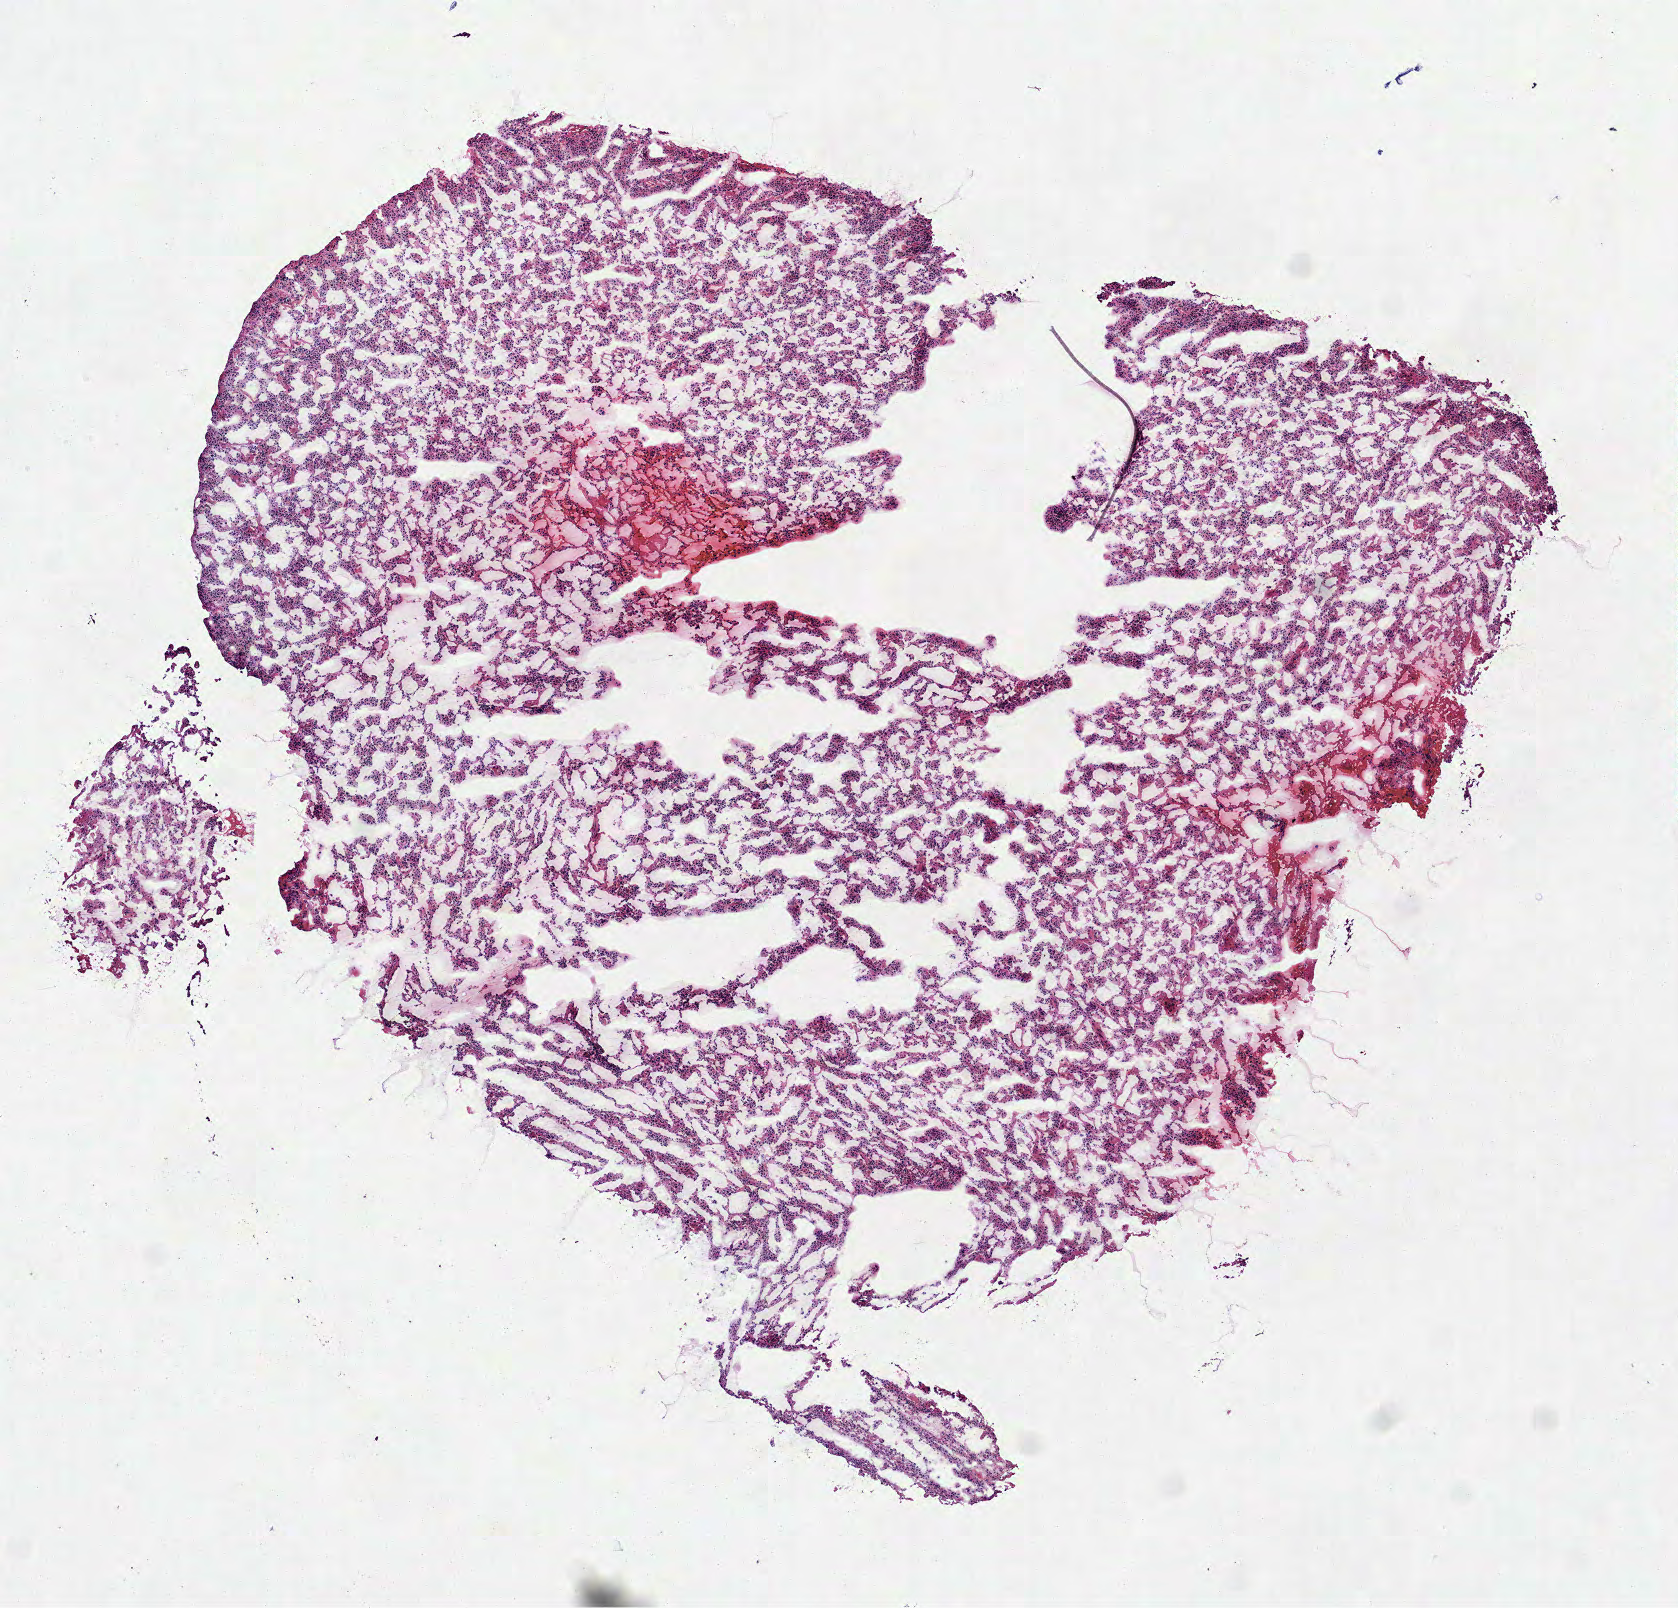
Digitized H&E tissue section (whole slide) — whole scanned area (about 6.8 x 6.5 mm) shown as a low-resolution overview, frozen section from the top of the tissue portion, primary tumour sample from the brain. Male patient; age at initial diagnosis 60 years. Slide review estimates, as recorded: tumour cells 100%, tumour nuclei 85%, normal cells 0%, stromal cells 0%, necrosis 0%.
- histologic diagnosis: Glioblastoma